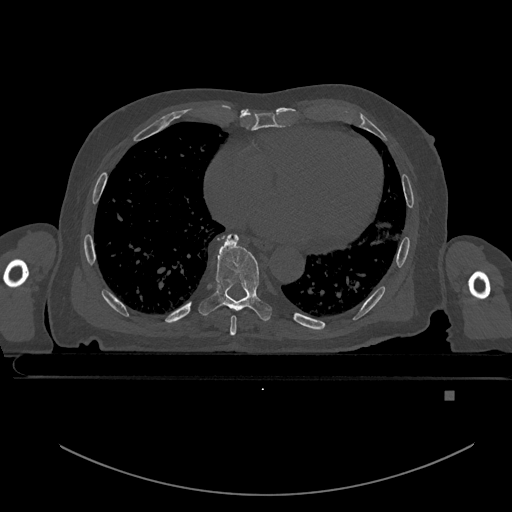
CT including the spine, one axial slice; position 209 of 969 along the scan axis; bone window (W 1800 / L 400 HU); 0.5 mm slice thickness; 512 × 512 image matrix, field of view 456 × 456 mm. Patient: male, 82 years. From the clinical record (not read from this slice): primary cancer: prostate; vertebrae with lytic lesions (as recorded): T11, T9, T8, T2.
Structures marked on this image (semi-automatic segmentation, software-assisted and operator-edited):
- T7 vertebra: bounding box <230,315,237,335> (left, top, right, bottom; pixels)
- T8 vertebra: <198,234,273,321>